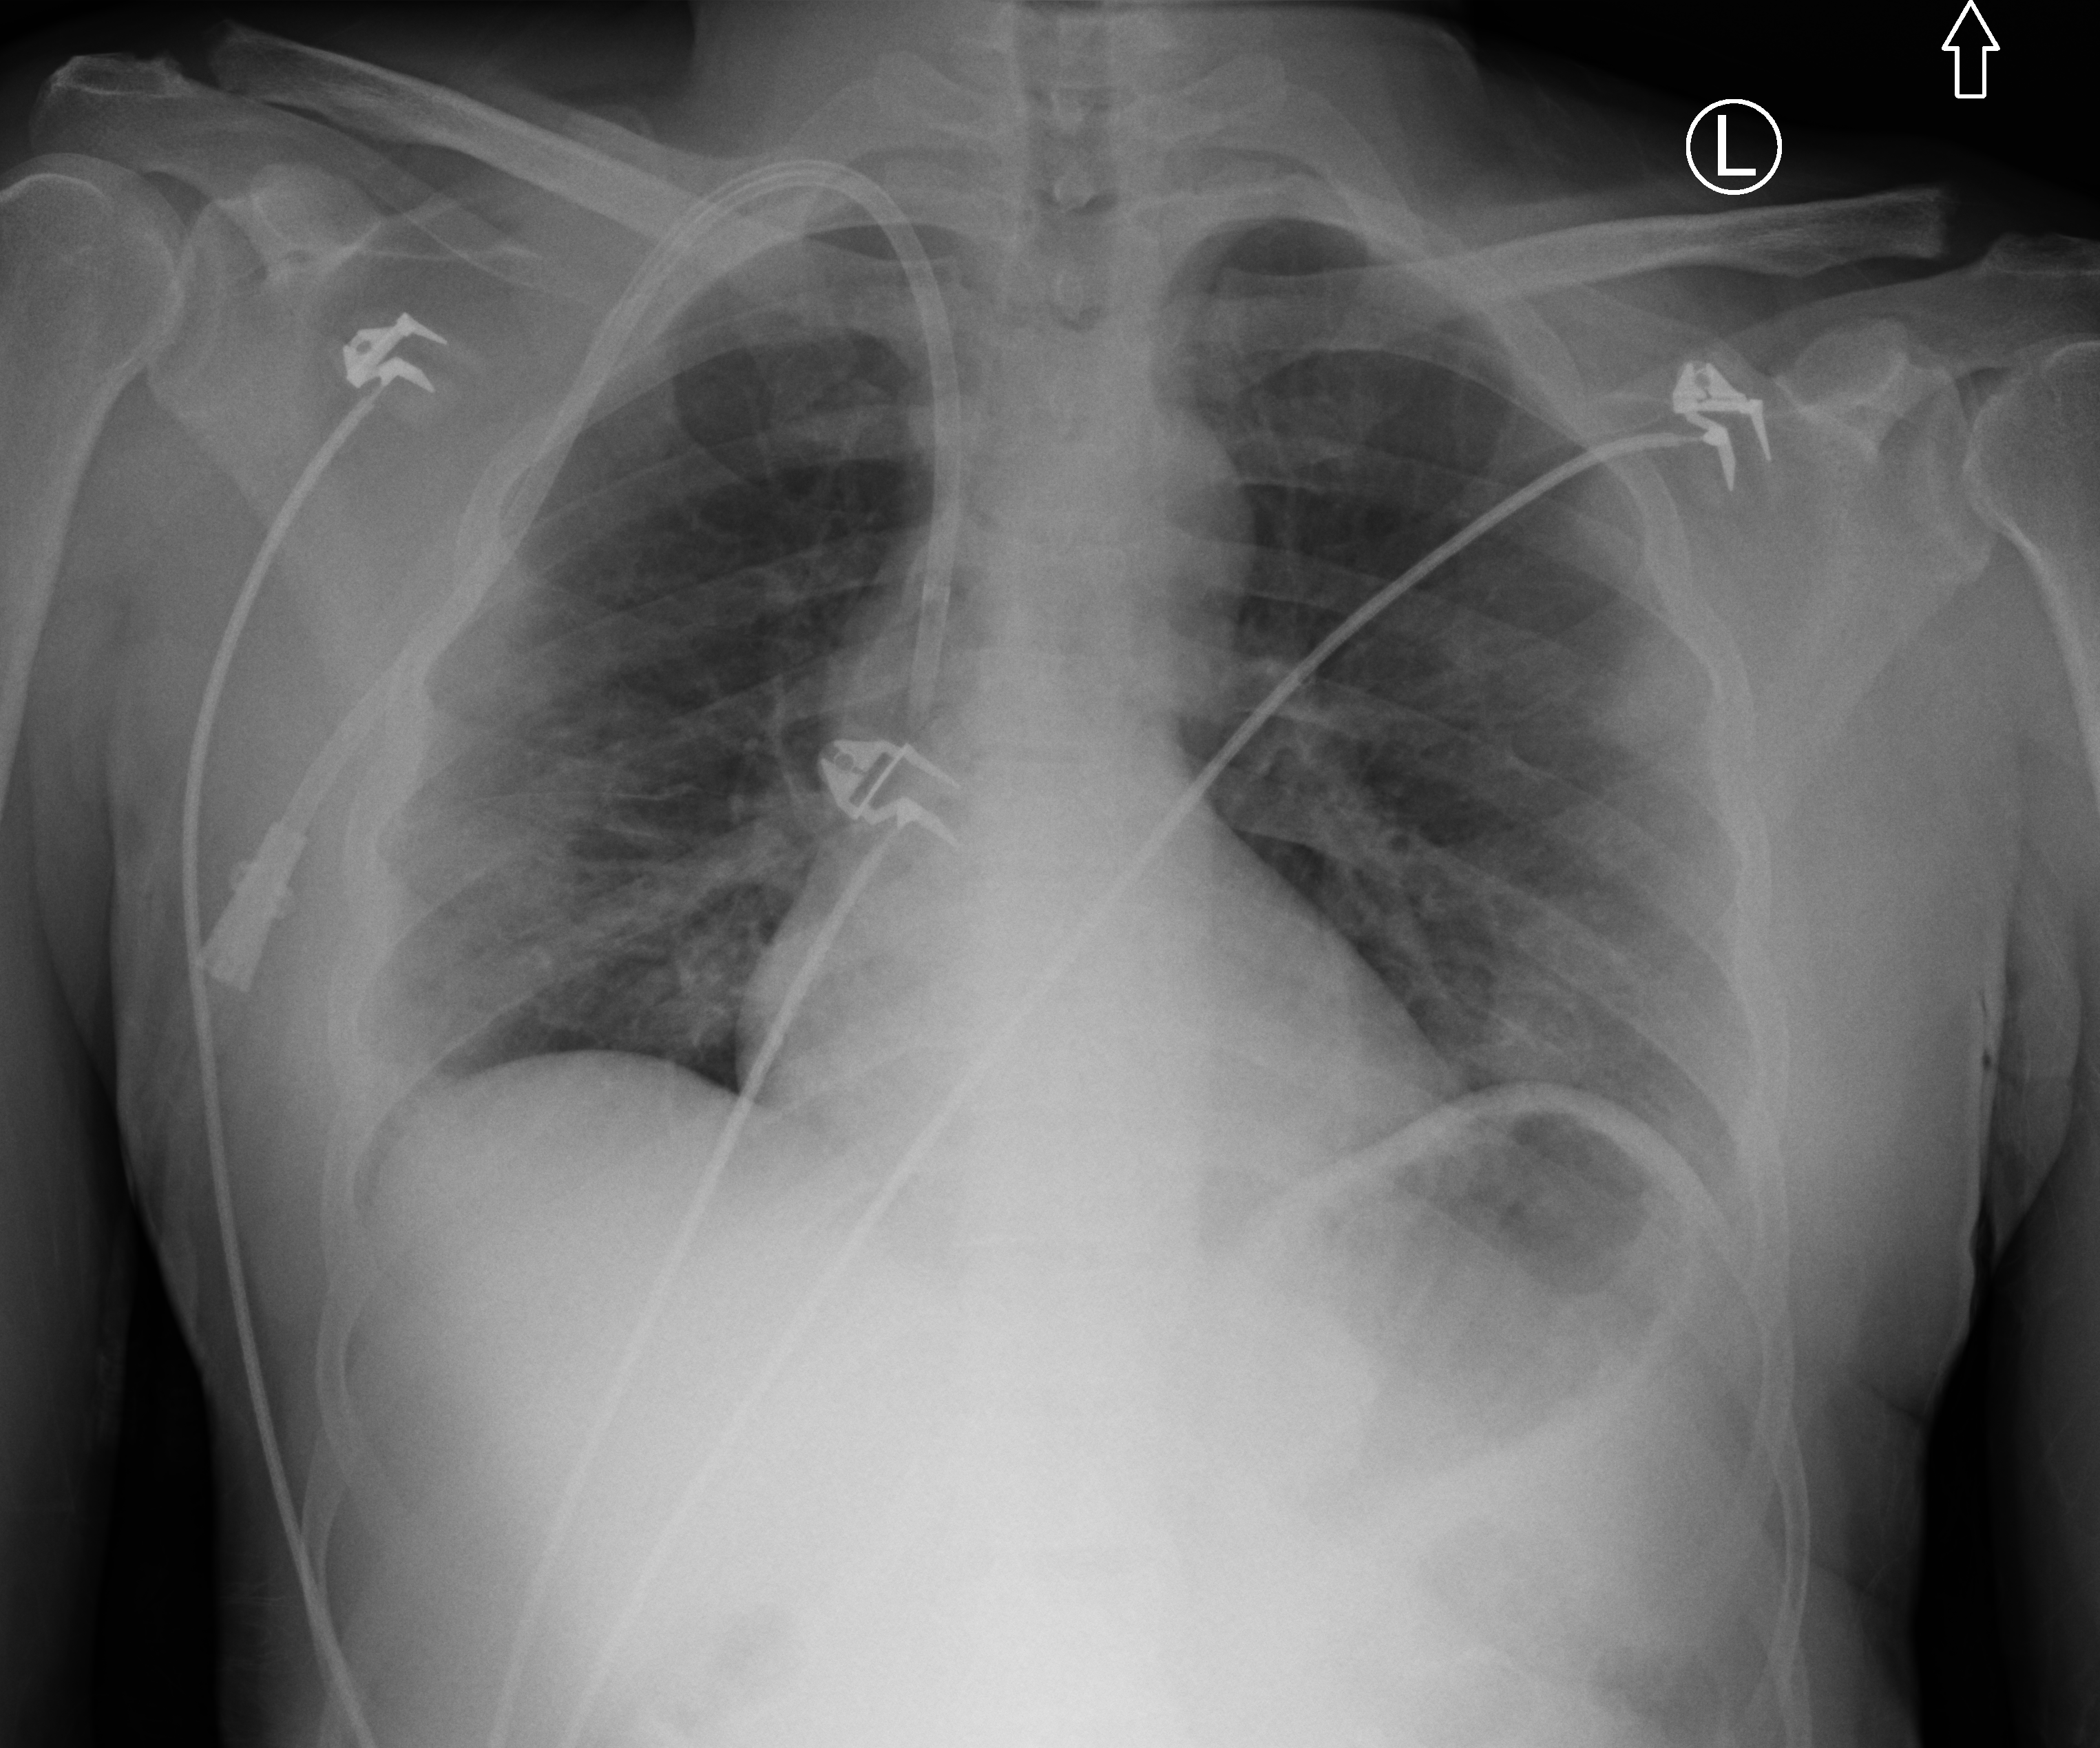
Chest X-ray (portable), anteroposterior (AP) projection. Patient hospitalised with COVID-19; male, aged 18–59 years.
Hospital-stay facts (about this admission, not read from this image; timing relative to this image not recorded): admitted to intensive care during this hospital stay: no; mechanically ventilated during this hospital stay: no.